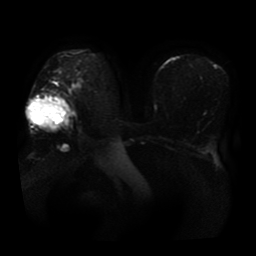
Breast MRI, one axial slice; position 27 of 41 along the scan axis; diffusion-weighted series; image 2 of 4 stored at this slice position (different b-values; order by instance number); 1.5 T; 5 mm slice thickness; 256 × 256 image matrix, field of view 360 × 360 mm. Female patient.
Structures marked on this image (manually delineated by an expert):
- tumour on diffusion-weighted imaging: box from (x=27, y=103) to (x=64, y=127) px